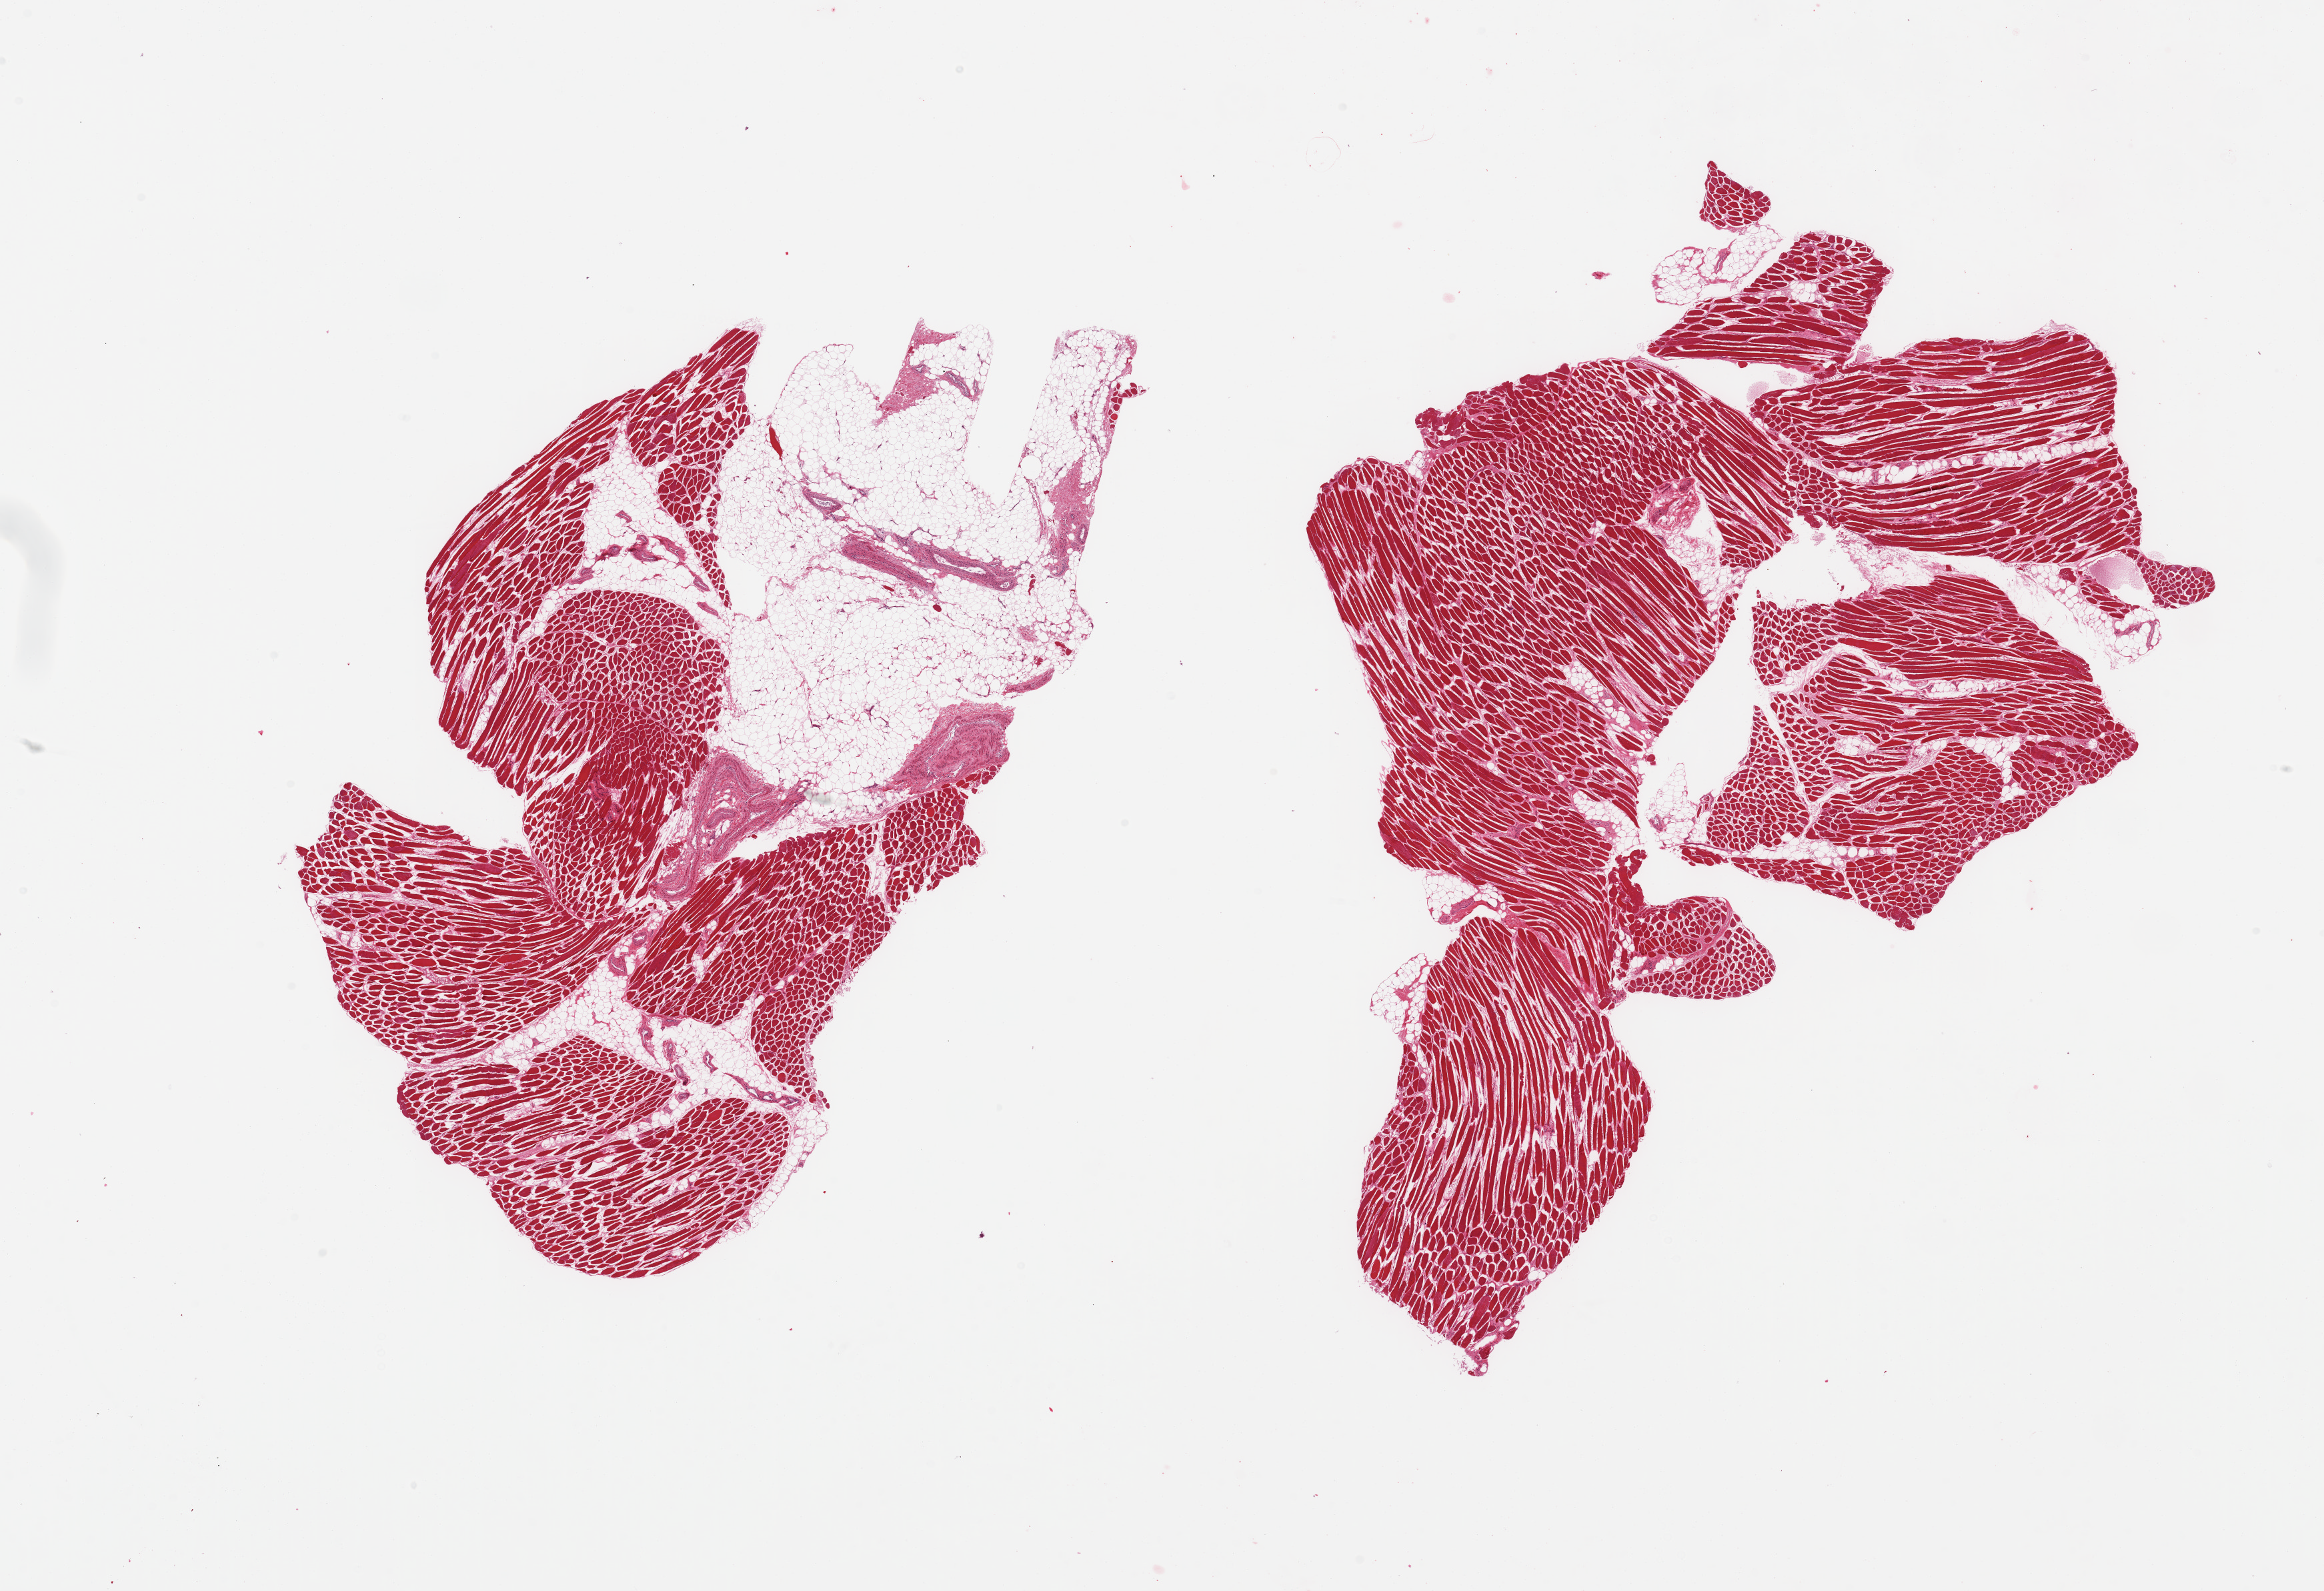
Hematoxylin and eosin (H&E) whole-slide image, low-resolution overview of the scanned area, about 27.6 x 18.9 mm, PAXgene-fixed, paraffin-embedded tissue, target tissue: skeletal muscle, tissue donor sample.
- pathologist's review note for this sample: 2 pieces, ~30% adherent/interstitial fat/vascular elements